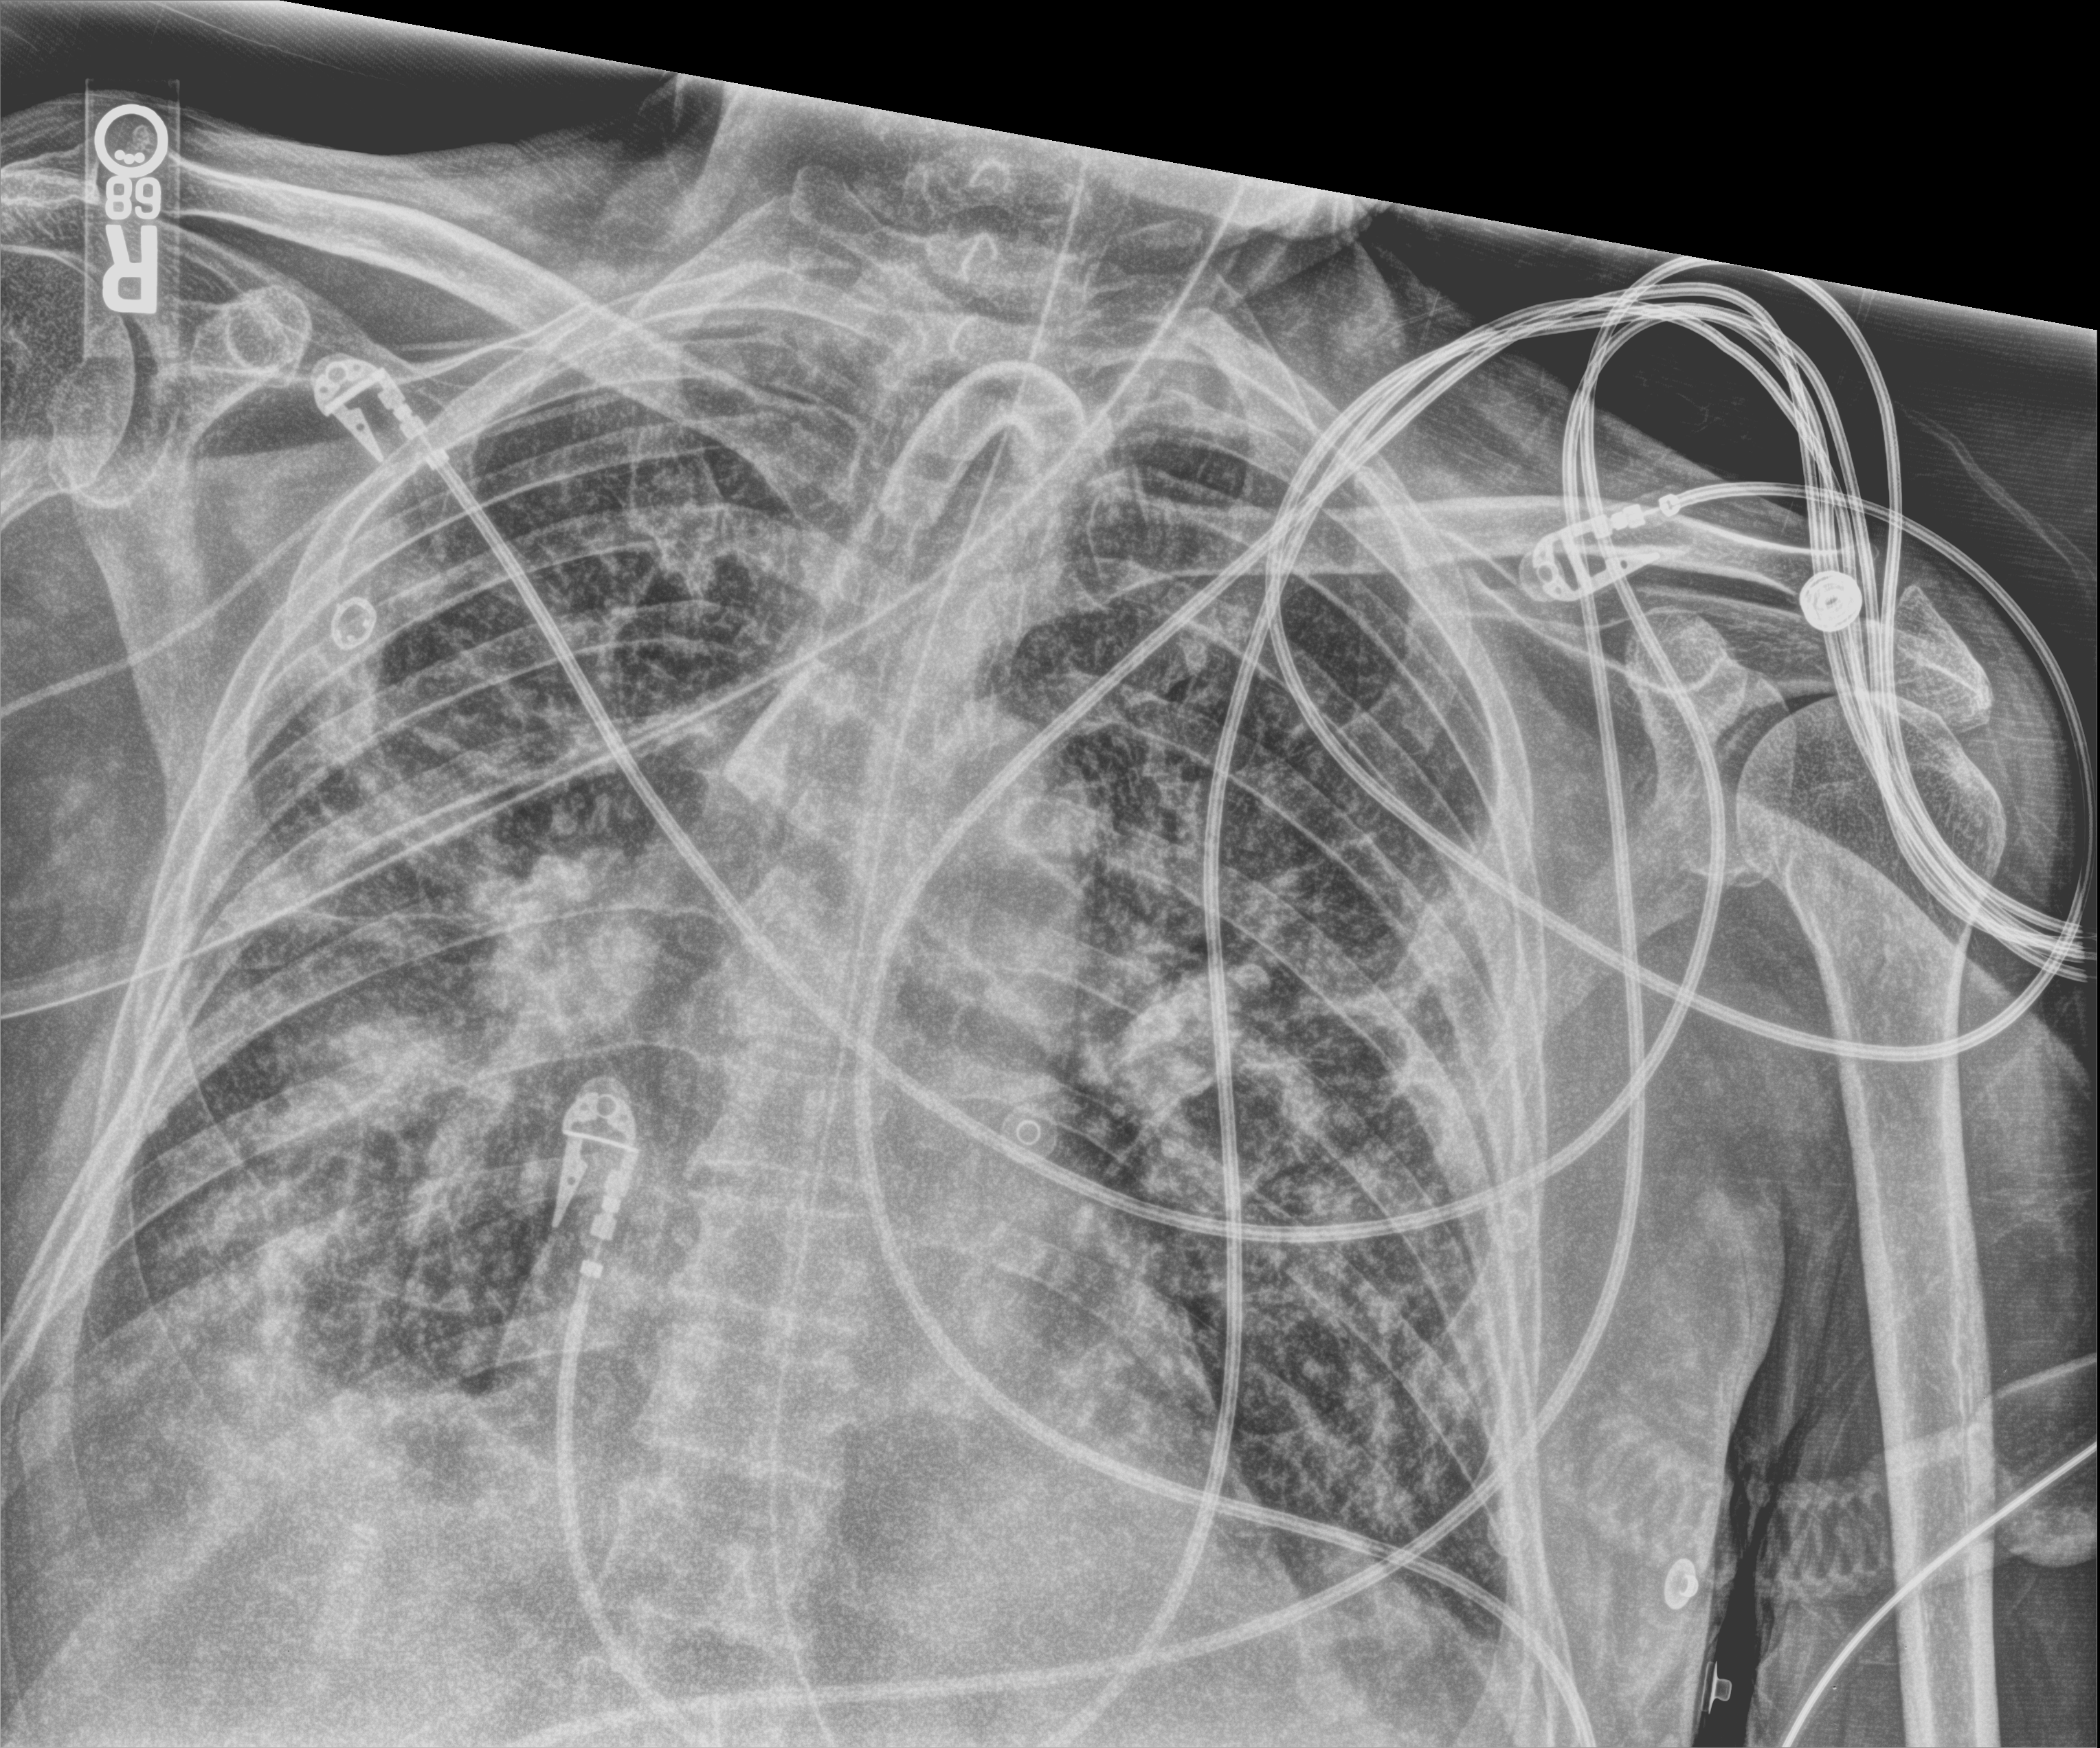
Portable chest radiograph, anteroposterior (AP) projection. Patient hospitalised with COVID-19; male, aged 75–90 years.
From the hospital-stay record, not from the radiograph (when in the stay this image was taken is not recorded):
- length of hospital stay: 70 days
- mechanically ventilated during this hospital stay: yes